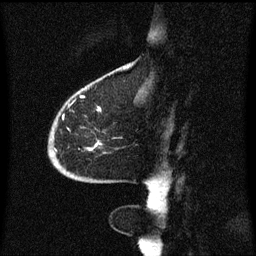
Breast MRI (dynamic contrast-enhanced), one sagittal slice. Slice 18 of 60 in the series (ordered by position). Dynamic contrast-enhanced series, image 2 of 3 at this slice position (ordered by acquisition). 1.5 T. TE 4.2 ms, TR 8.4 ms. 2 mm slice thickness. 256 × 256 image matrix. Patient: female, 68 years. Case-level facts recorded for this patient, not image findings: setting: breast cancer imaged before/during neoadjuvant chemotherapy; receptor status: triple-negative.
Outlined on this slice (semi-automatically segmented with operator editing):
- analysis volume of interest (the breast-tissue region the enhancement analysis was run in; not a lesion): bounding box [x1, y1, x2, y2] px = [49, 94, 102, 173]
- tumour enhancement mask (voxels above the 70 % enhancement threshold inside the analysis volume of interest): [56, 108, 102, 167]